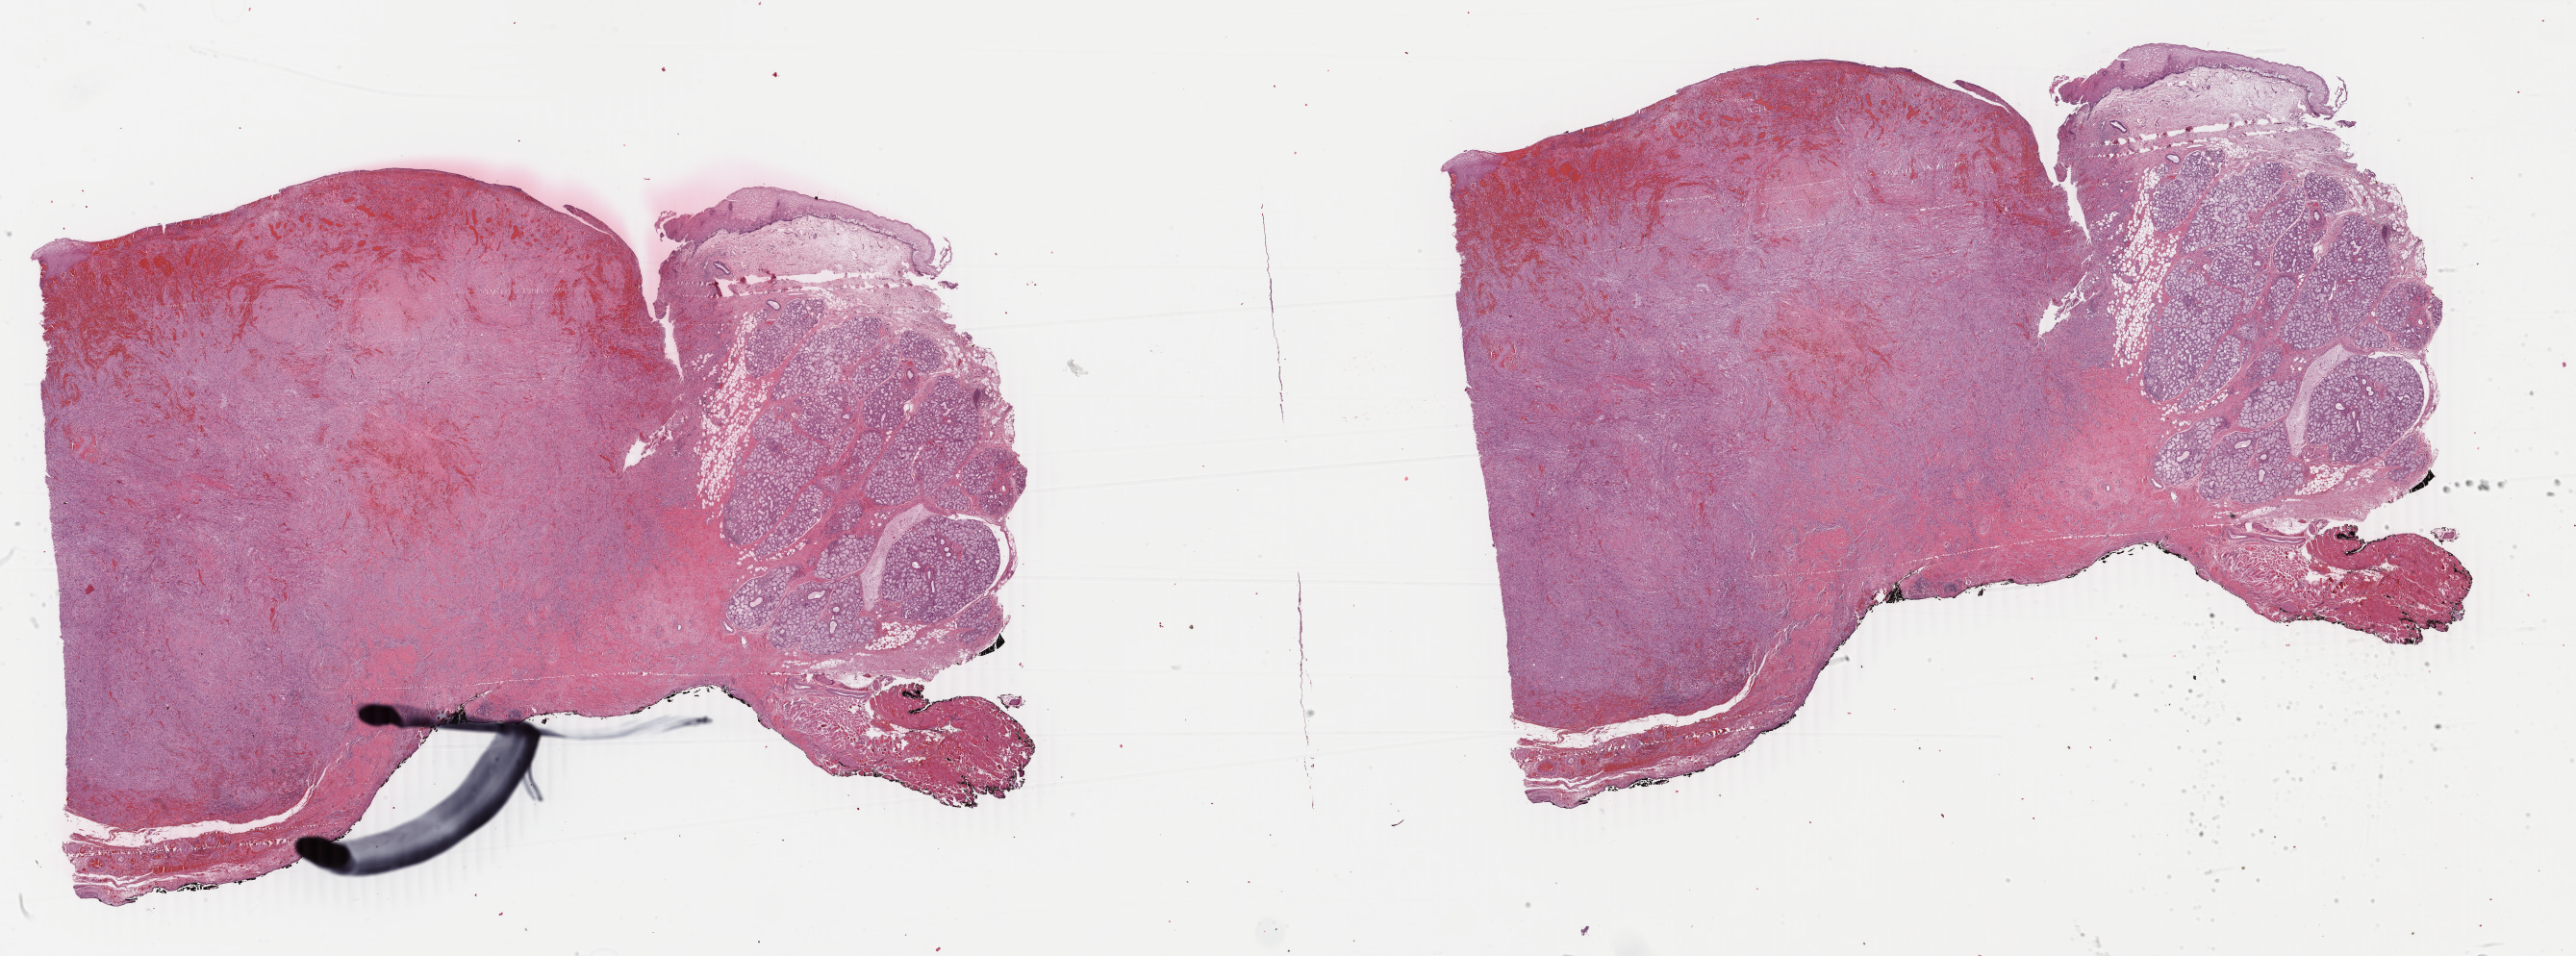
H&E-stained whole-slide image, shown as a low-resolution overview of the whole scanned area (about 42.6 x 15.8 mm); formalin-fixed paraffin-embedded (FFPE) diagnostic section; sample: primary tumour, head and neck. Male patient; age at initial diagnosis 43 years. Histologic grade: GX (grade cannot be assessed).
AJCC pathologic stage: IVA (7th edition). TNM: T2 N2b MX. Histologic diagnosis: Squamous cell carcinoma, spindle cell (base of tongue, NOS). Laterality: right.